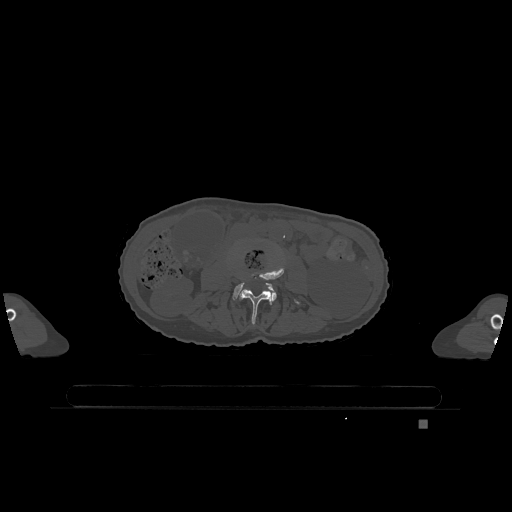
CT including the spine, one axial slice. Bone window (W 1800 / L 400 HU). 0.5 mm slice thickness. 512 × 512 image matrix. Patient: female, 74 years. Case-level facts recorded for this patient, not image findings: primary cancer: lung; vertebrae with lytic lesions (as recorded): T1, T4, T5, T6, L4, L5.
Outlined on this slice (semi-automatically segmented with operator editing):
- L3 vertebra: bounding box [x1, y1, x2, y2] px = [238, 266, 300, 325]
- L4 vertebra: [233, 282, 277, 302]